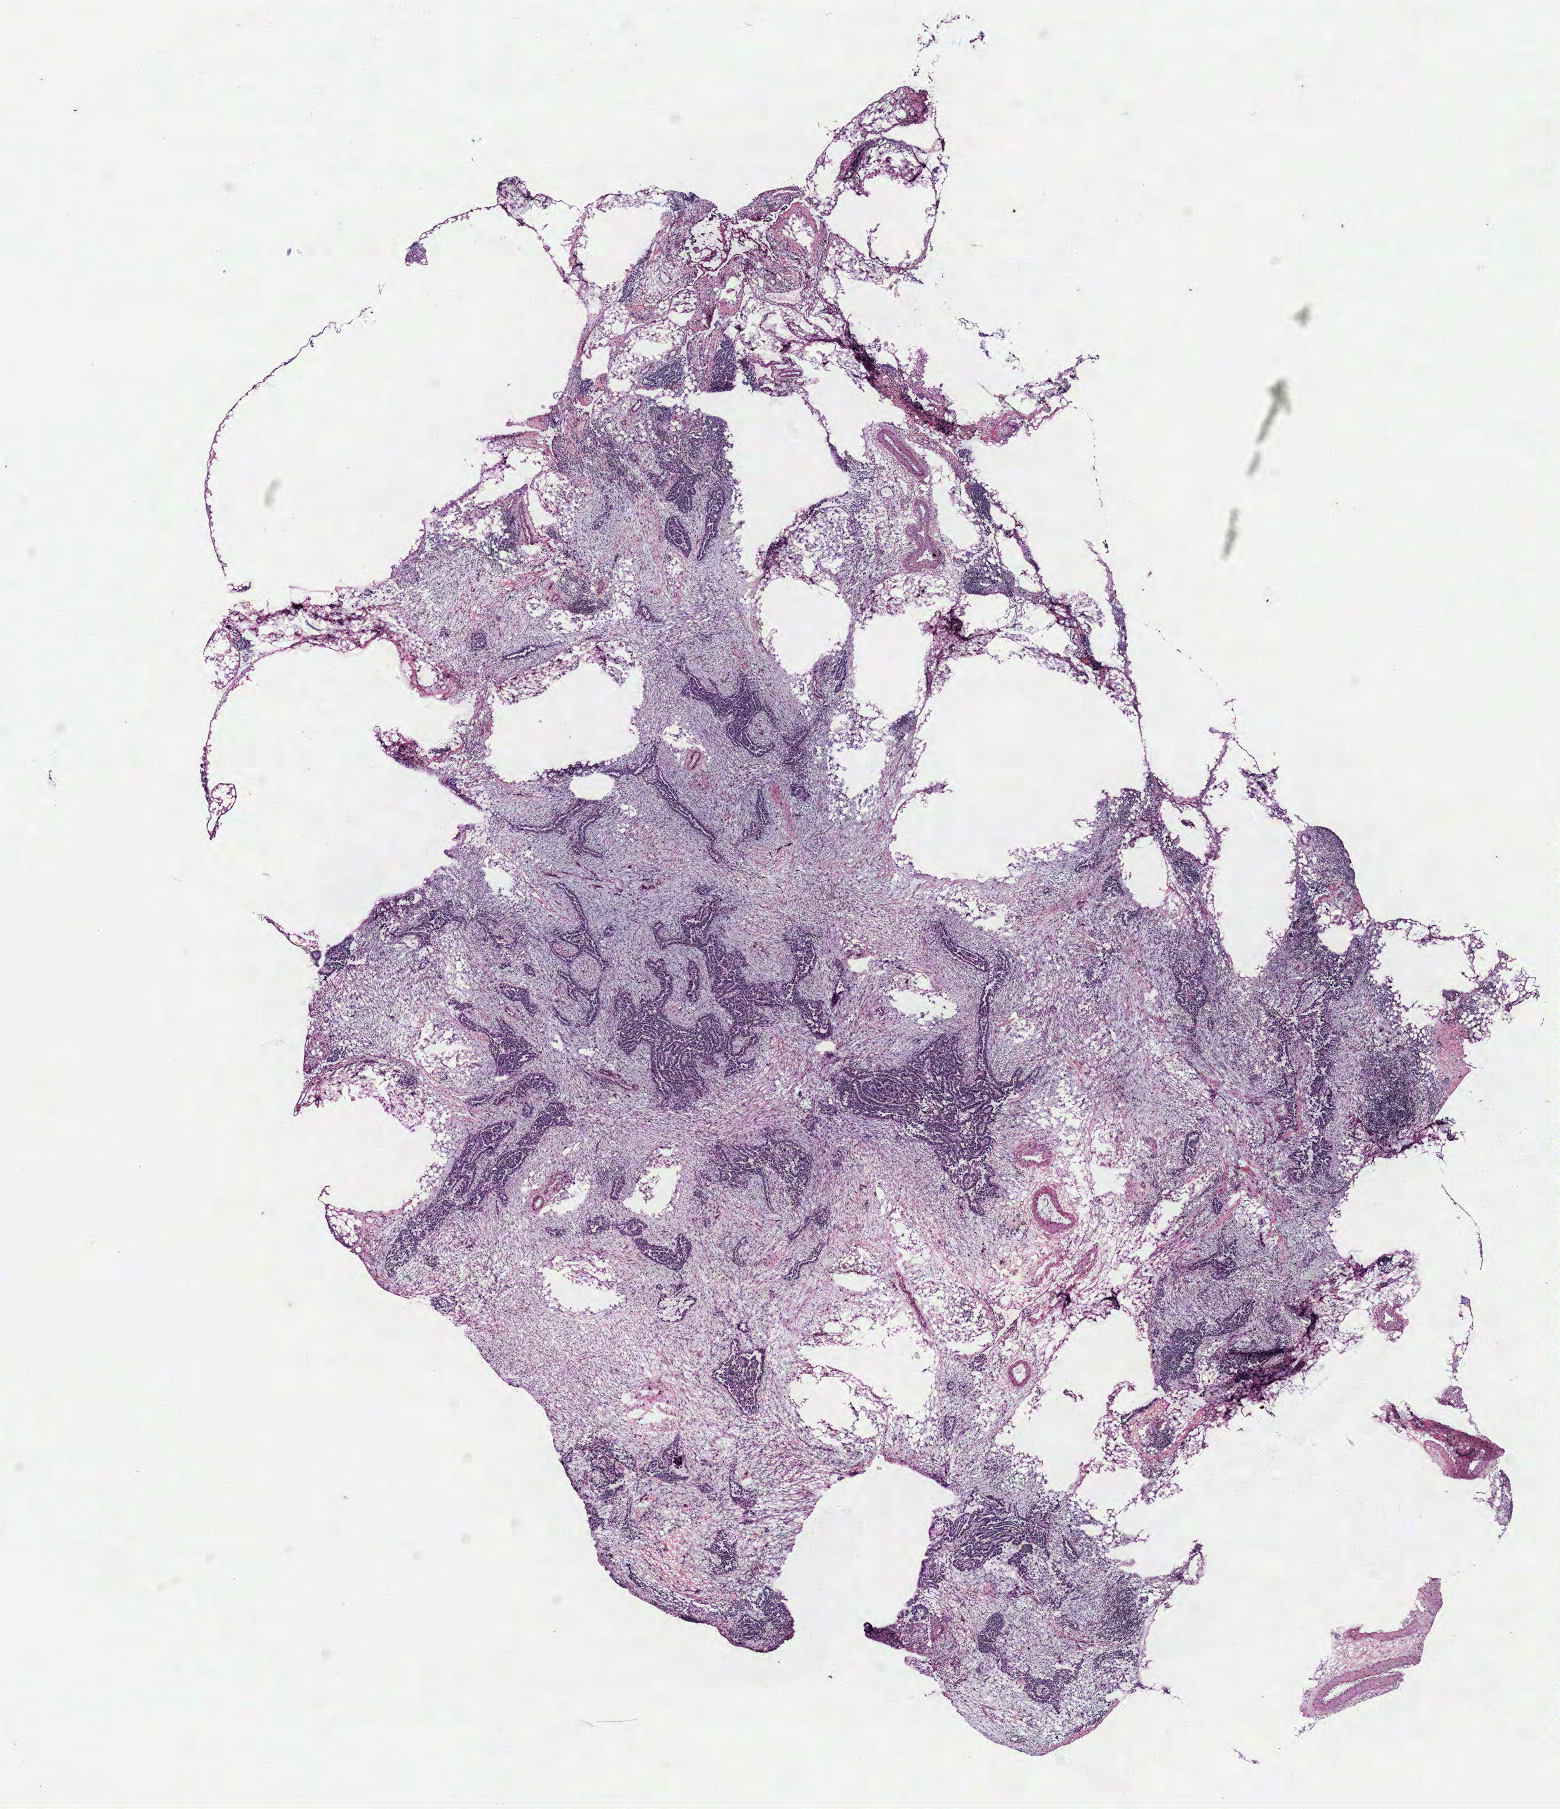
H&E-stained whole-slide image — a low-resolution overview of the entire scanned area, about 12.5 x 14.5 mm. Tumour tissue sample, ovary. 44-year-old female patient.
* primary tumour site (as recorded): fallopian tube
* diagnosis: Serous adenocarcinoma, NOS